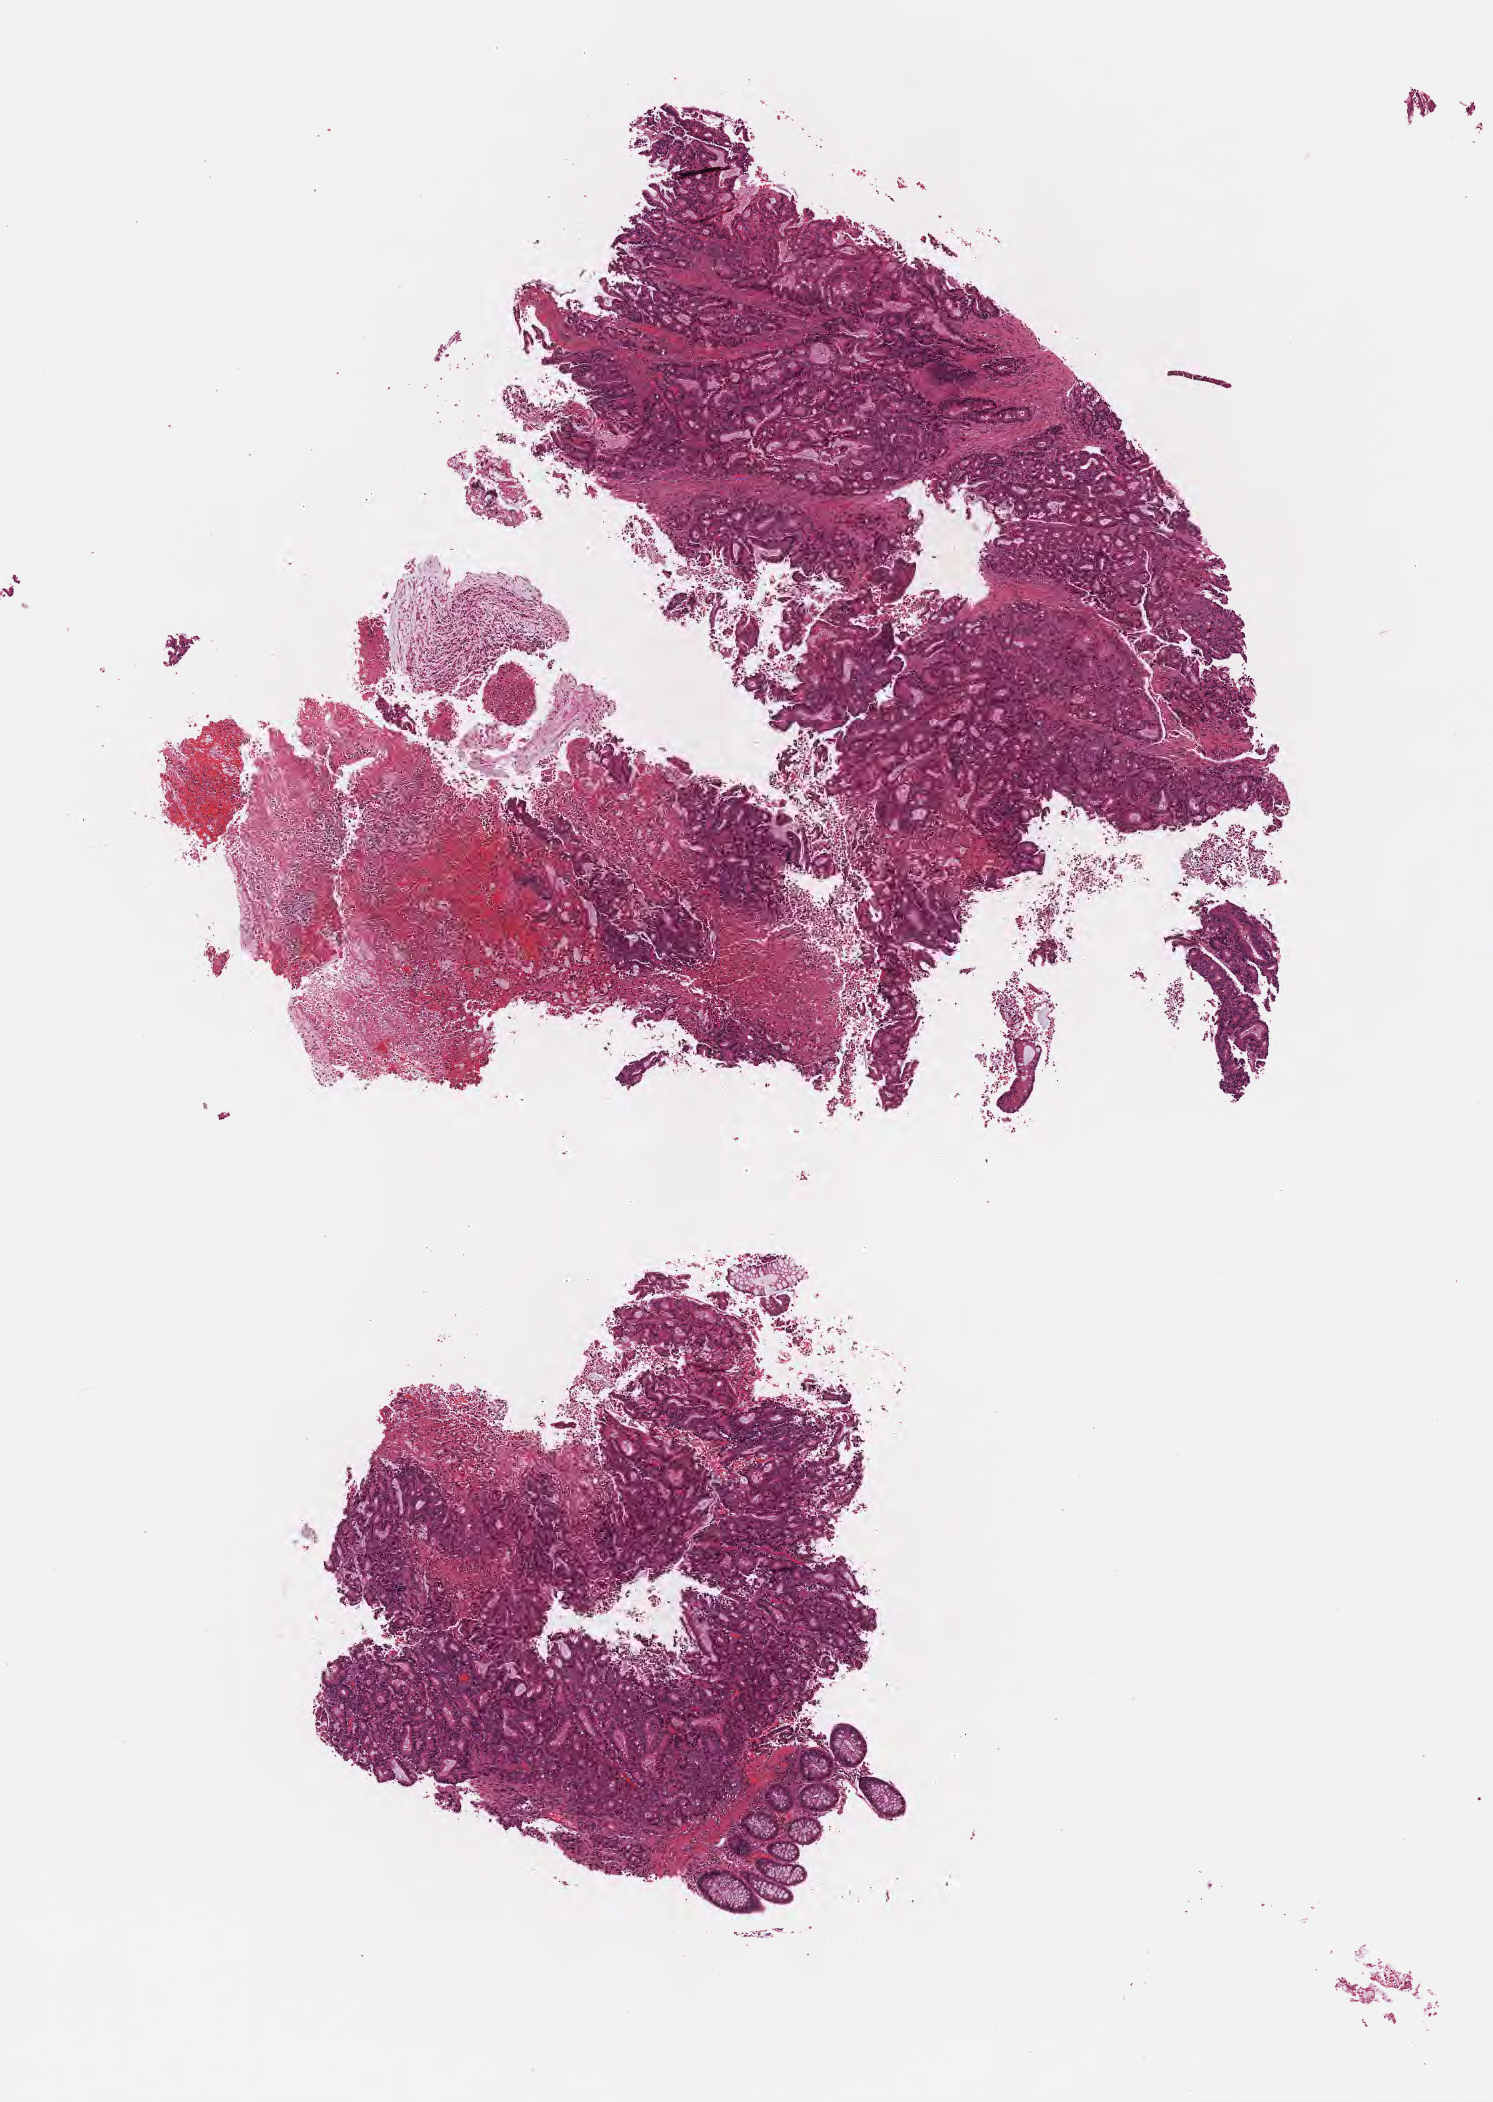
Digitized H&E-stained section — shown as a low-resolution overview of the whole scanned area (about 6.0 x 8.5 mm); formalin-fixed paraffin-embedded section; primary tumor; anatomic site: splenic flexure of colon. Male patient; age at initial diagnosis 72 years. Pathologist review of this section (percent, as recorded): tumor cells 80%, tumor nuclei 80%.
Histologic diagnosis: Adenocarcinoma, NOS.